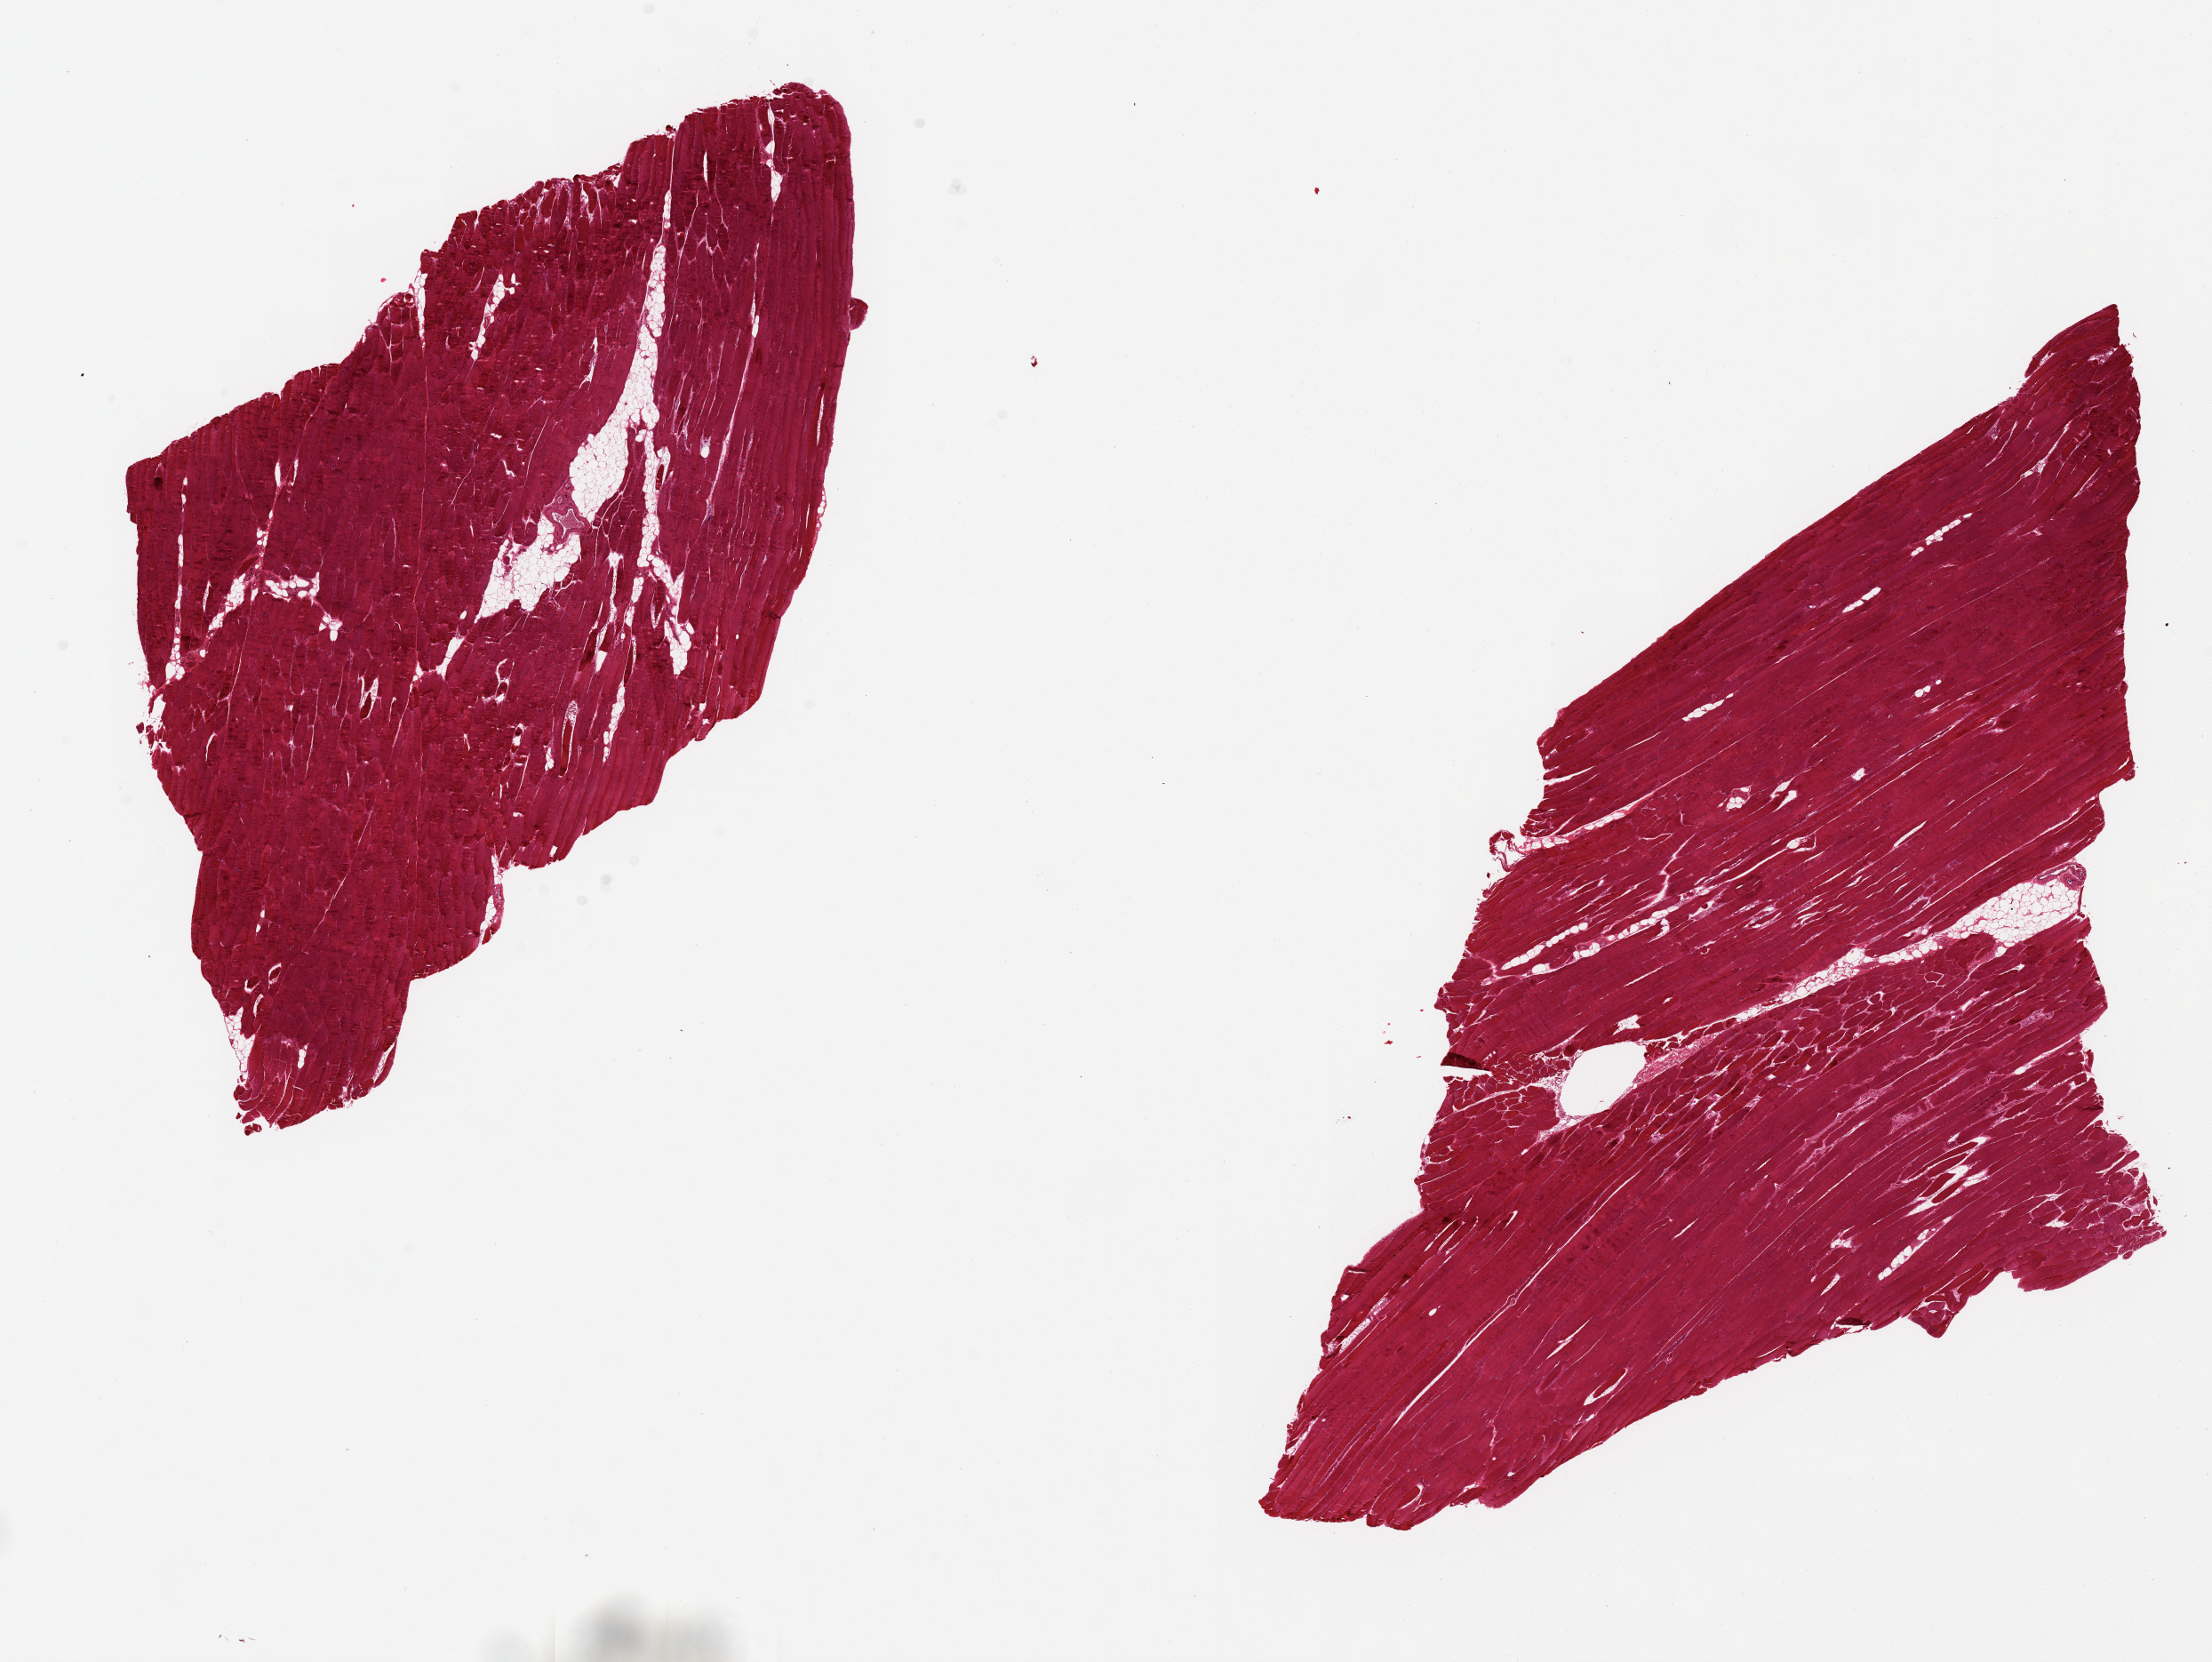
Haematoxylin and eosin whole-slide image — a low-resolution overview of the entire scanned area, about 19.7 x 14.8 mm (acquisition: 20x scan); PAXgene-fixed, paraffin-embedded tissue; section of skeletal muscle (target tissue); tissue donor sample. Male donor.
Review note (as recorded): 2 aliquots, ~9x7mm. Minimal interstital fat. Unusually poorly preserved.